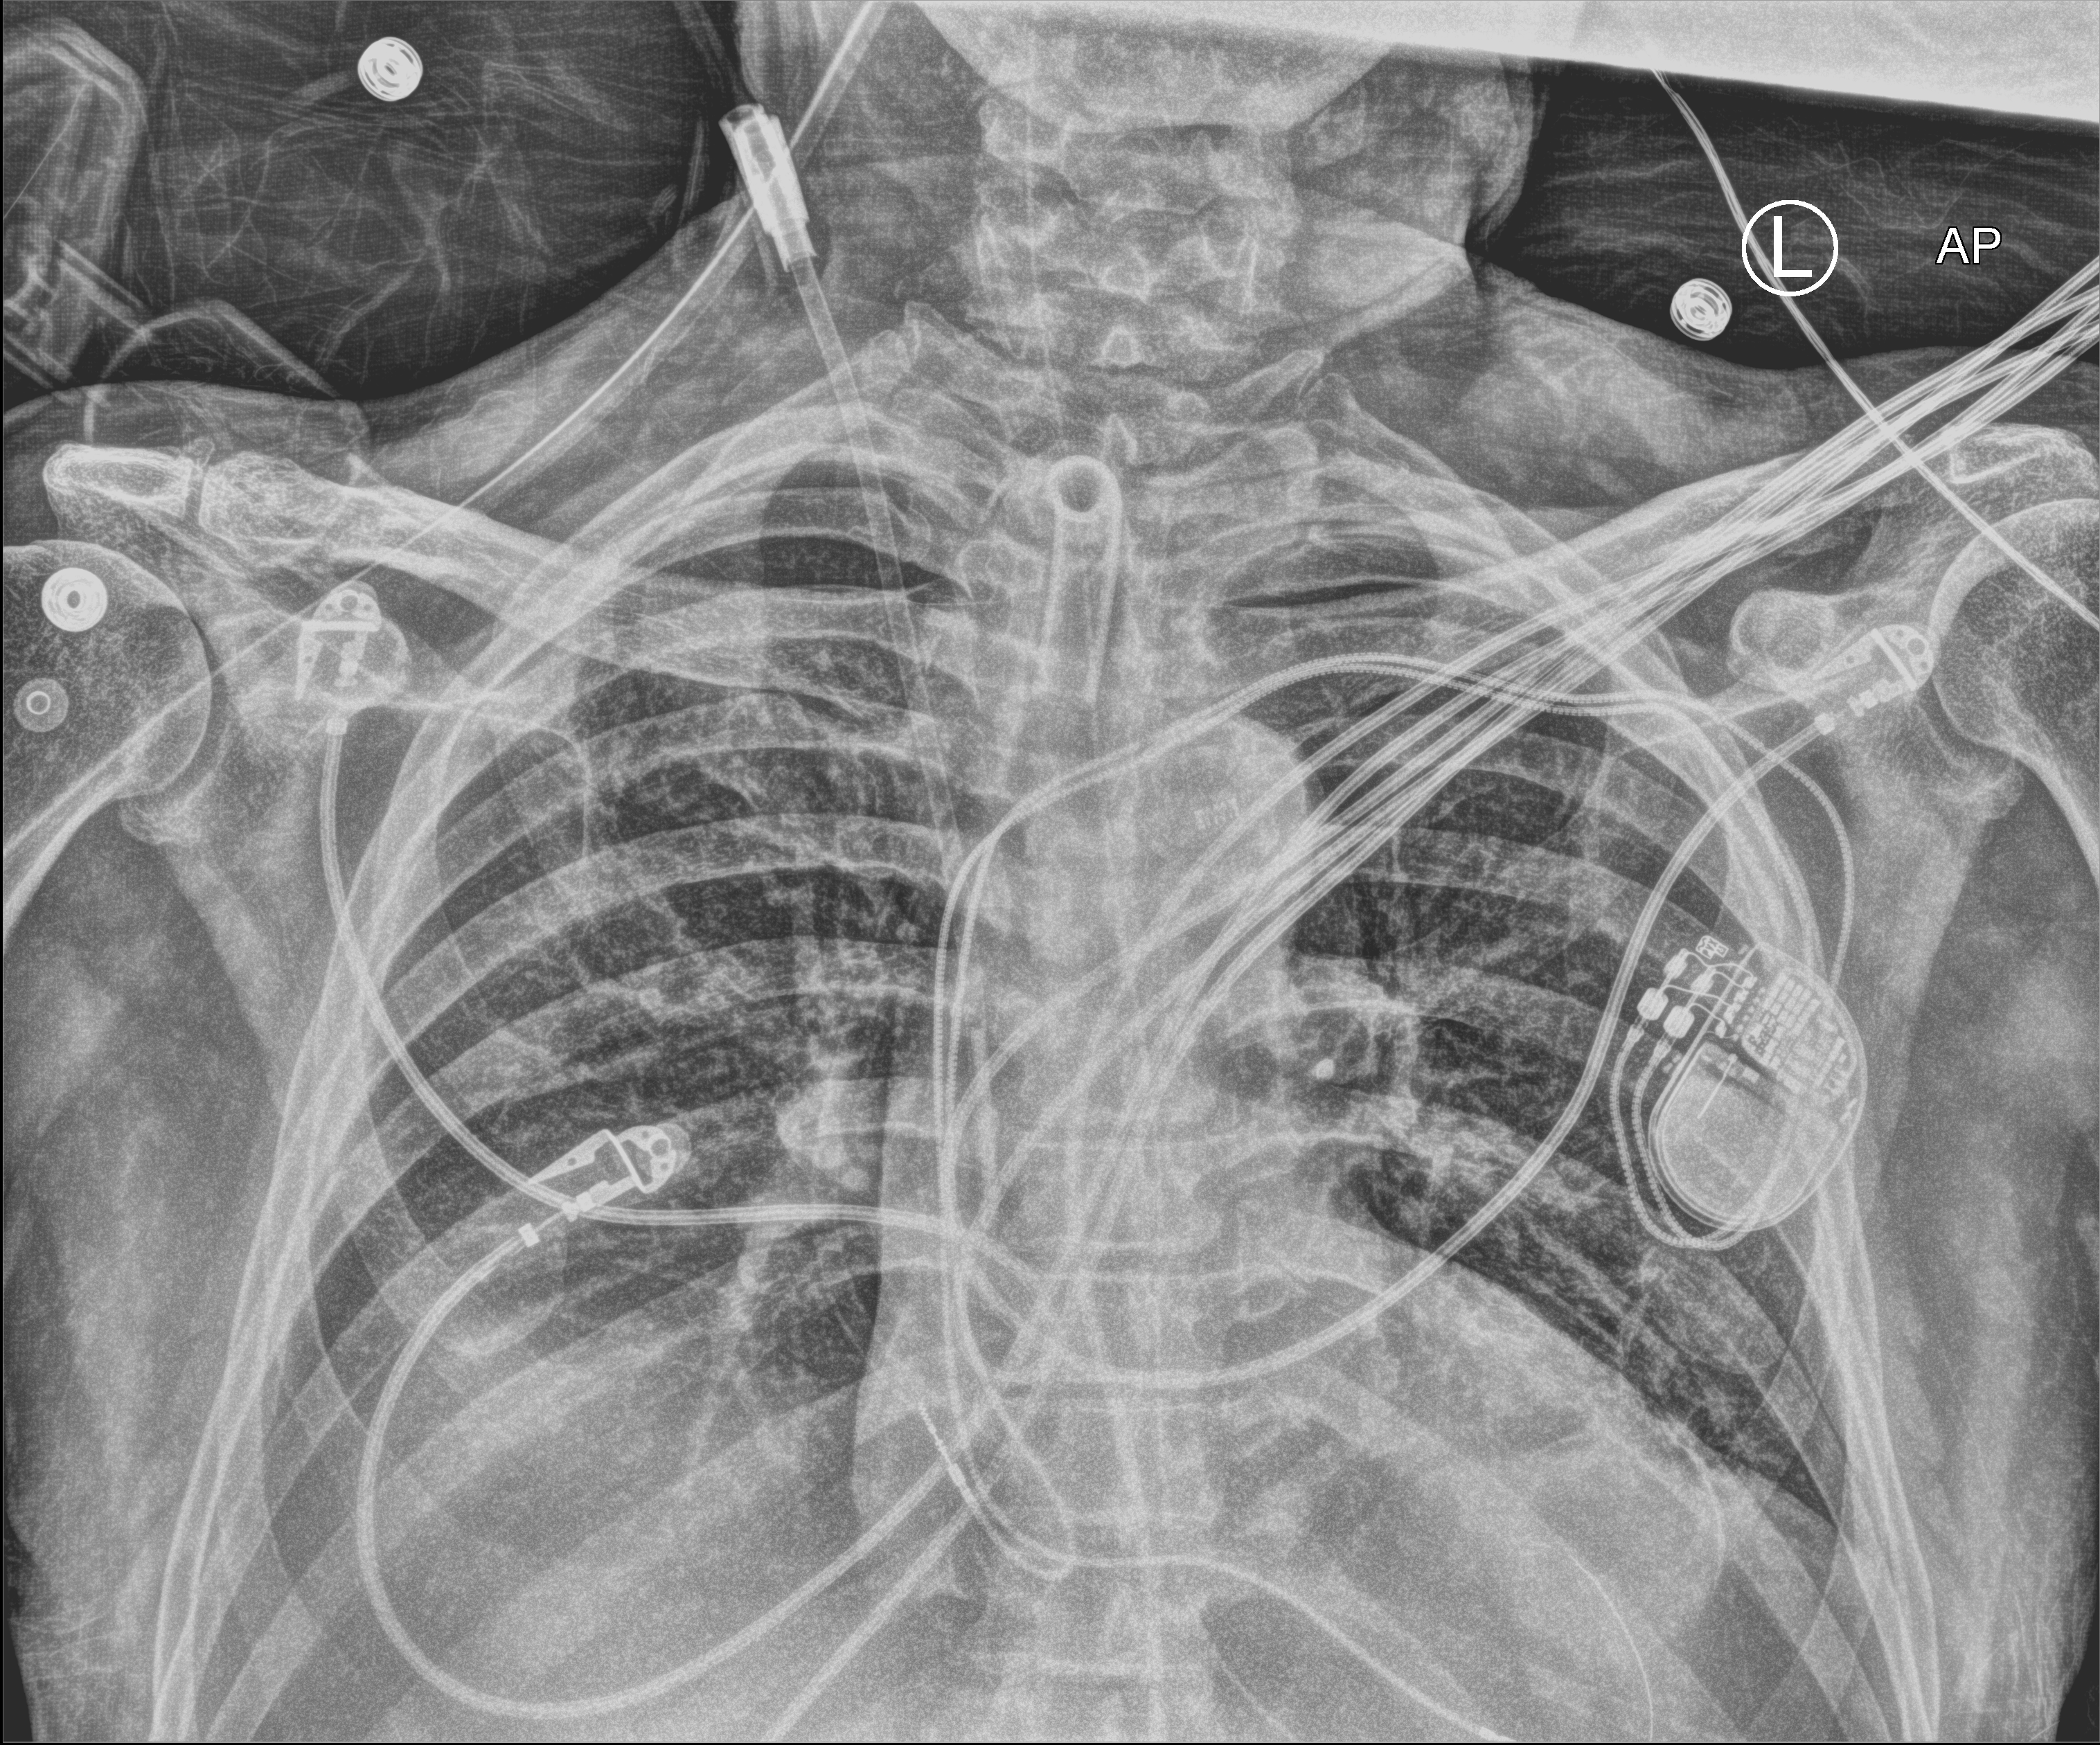
Chest X-ray (portable), anteroposterior (AP) projection. Patient hospitalised with COVID-19; male, aged 60–74 years.
Admission-level facts for this patient (not findings on this image; timing relative to this image not recorded): admitted to intensive care during this hospital stay: yes.